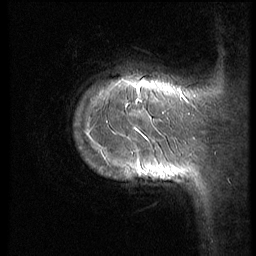
Breast MRI (dynamic contrast-enhanced), one sagittal slice; position 10 of 70 along the scan axis; 3 images stored at this slice position (order not interpretable as contrast timing); 1.5 T; TE 4.2 ms, TR 9 ms; 2.5 mm slice thickness; 256 × 256 image matrix, field of view 180 × 180 mm. Female patient, age 28 years. From the clinical record (not read from this slice): setting: breast cancer imaged before/during neoadjuvant chemotherapy.
Annotated regions visible in this slice (semi-automatically segmented with operator editing):
- analysis volume of interest (the breast-tissue region the enhancement analysis was run in; not a lesion): bounding box [x1, y1, x2, y2] px = [70, 47, 186, 213]
- tumour enhancement mask (voxels above the 140 % enhancement threshold inside the analysis volume of interest): [126, 86, 171, 180]